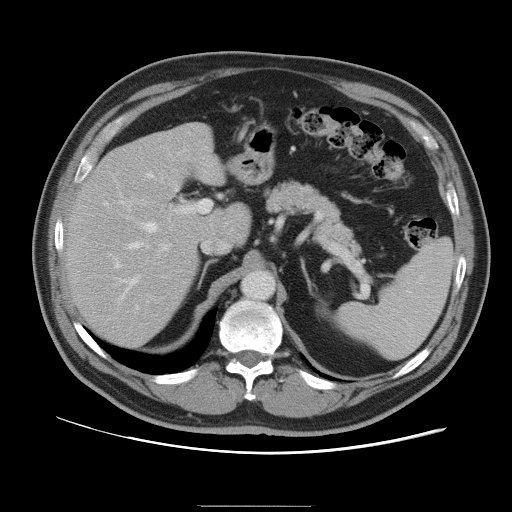
Contrast-enhanced abdominal CT, one axial slice; slice 64 of 105 in the series (ordered by position); 120 kVp; intravenous contrast given; soft-tissue window (W 400 / L 40 HU); 5 mm slice thickness; 512 × 512 image matrix, field of view 399 × 399 mm. Male patient, age 64 years. From the clinical record (not read from this slice): diagnosis: colorectal cancer liver metastases, imaged before liver resection; multiple liver metastases: yes; largest metastasis: 3 cm; disease in both lobes: yes.
Structures marked on this image (outlined manually by an expert reader):
- hepatic veins: box from (x=129, y=173) to (x=157, y=285) px
- liver: (x=65, y=123)–(x=249, y=346)
- planned liver remnant (the part of the liver to remain after resection): (x=66, y=136)–(x=249, y=346)
- portal vein (with intrahepatic branches): (x=115, y=200)–(x=212, y=314)